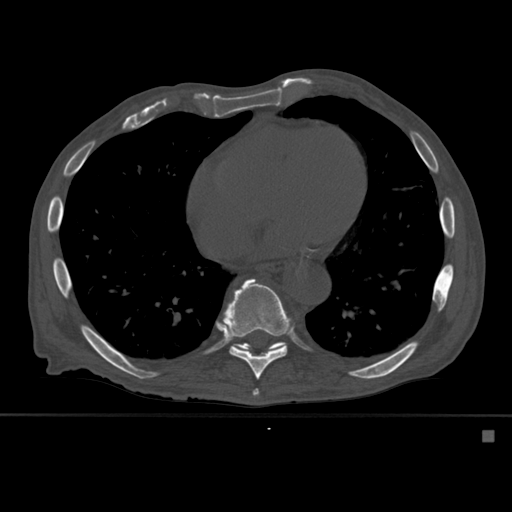
CT including the spine, one axial slice; slice 330 of 527 in the series (ordered by position); bone window (W 1800 / L 400 HU); 1.5 mm slice thickness; 512 × 512 image matrix, field of view 373 × 373 mm. Male patient, age 78 years. From the clinical record (not read from this slice): primary cancer: prostate.
Annotated regions visible in this slice (semi-automatic segmentation, software-assisted and operator-edited):
- T10 vertebra: bounding box (x1, y1, x2, y2) in pixels: (232, 343, 283, 351)
- T8 vertebra: (253, 389, 259, 396)
- T9 vertebra: (222, 278, 294, 380)